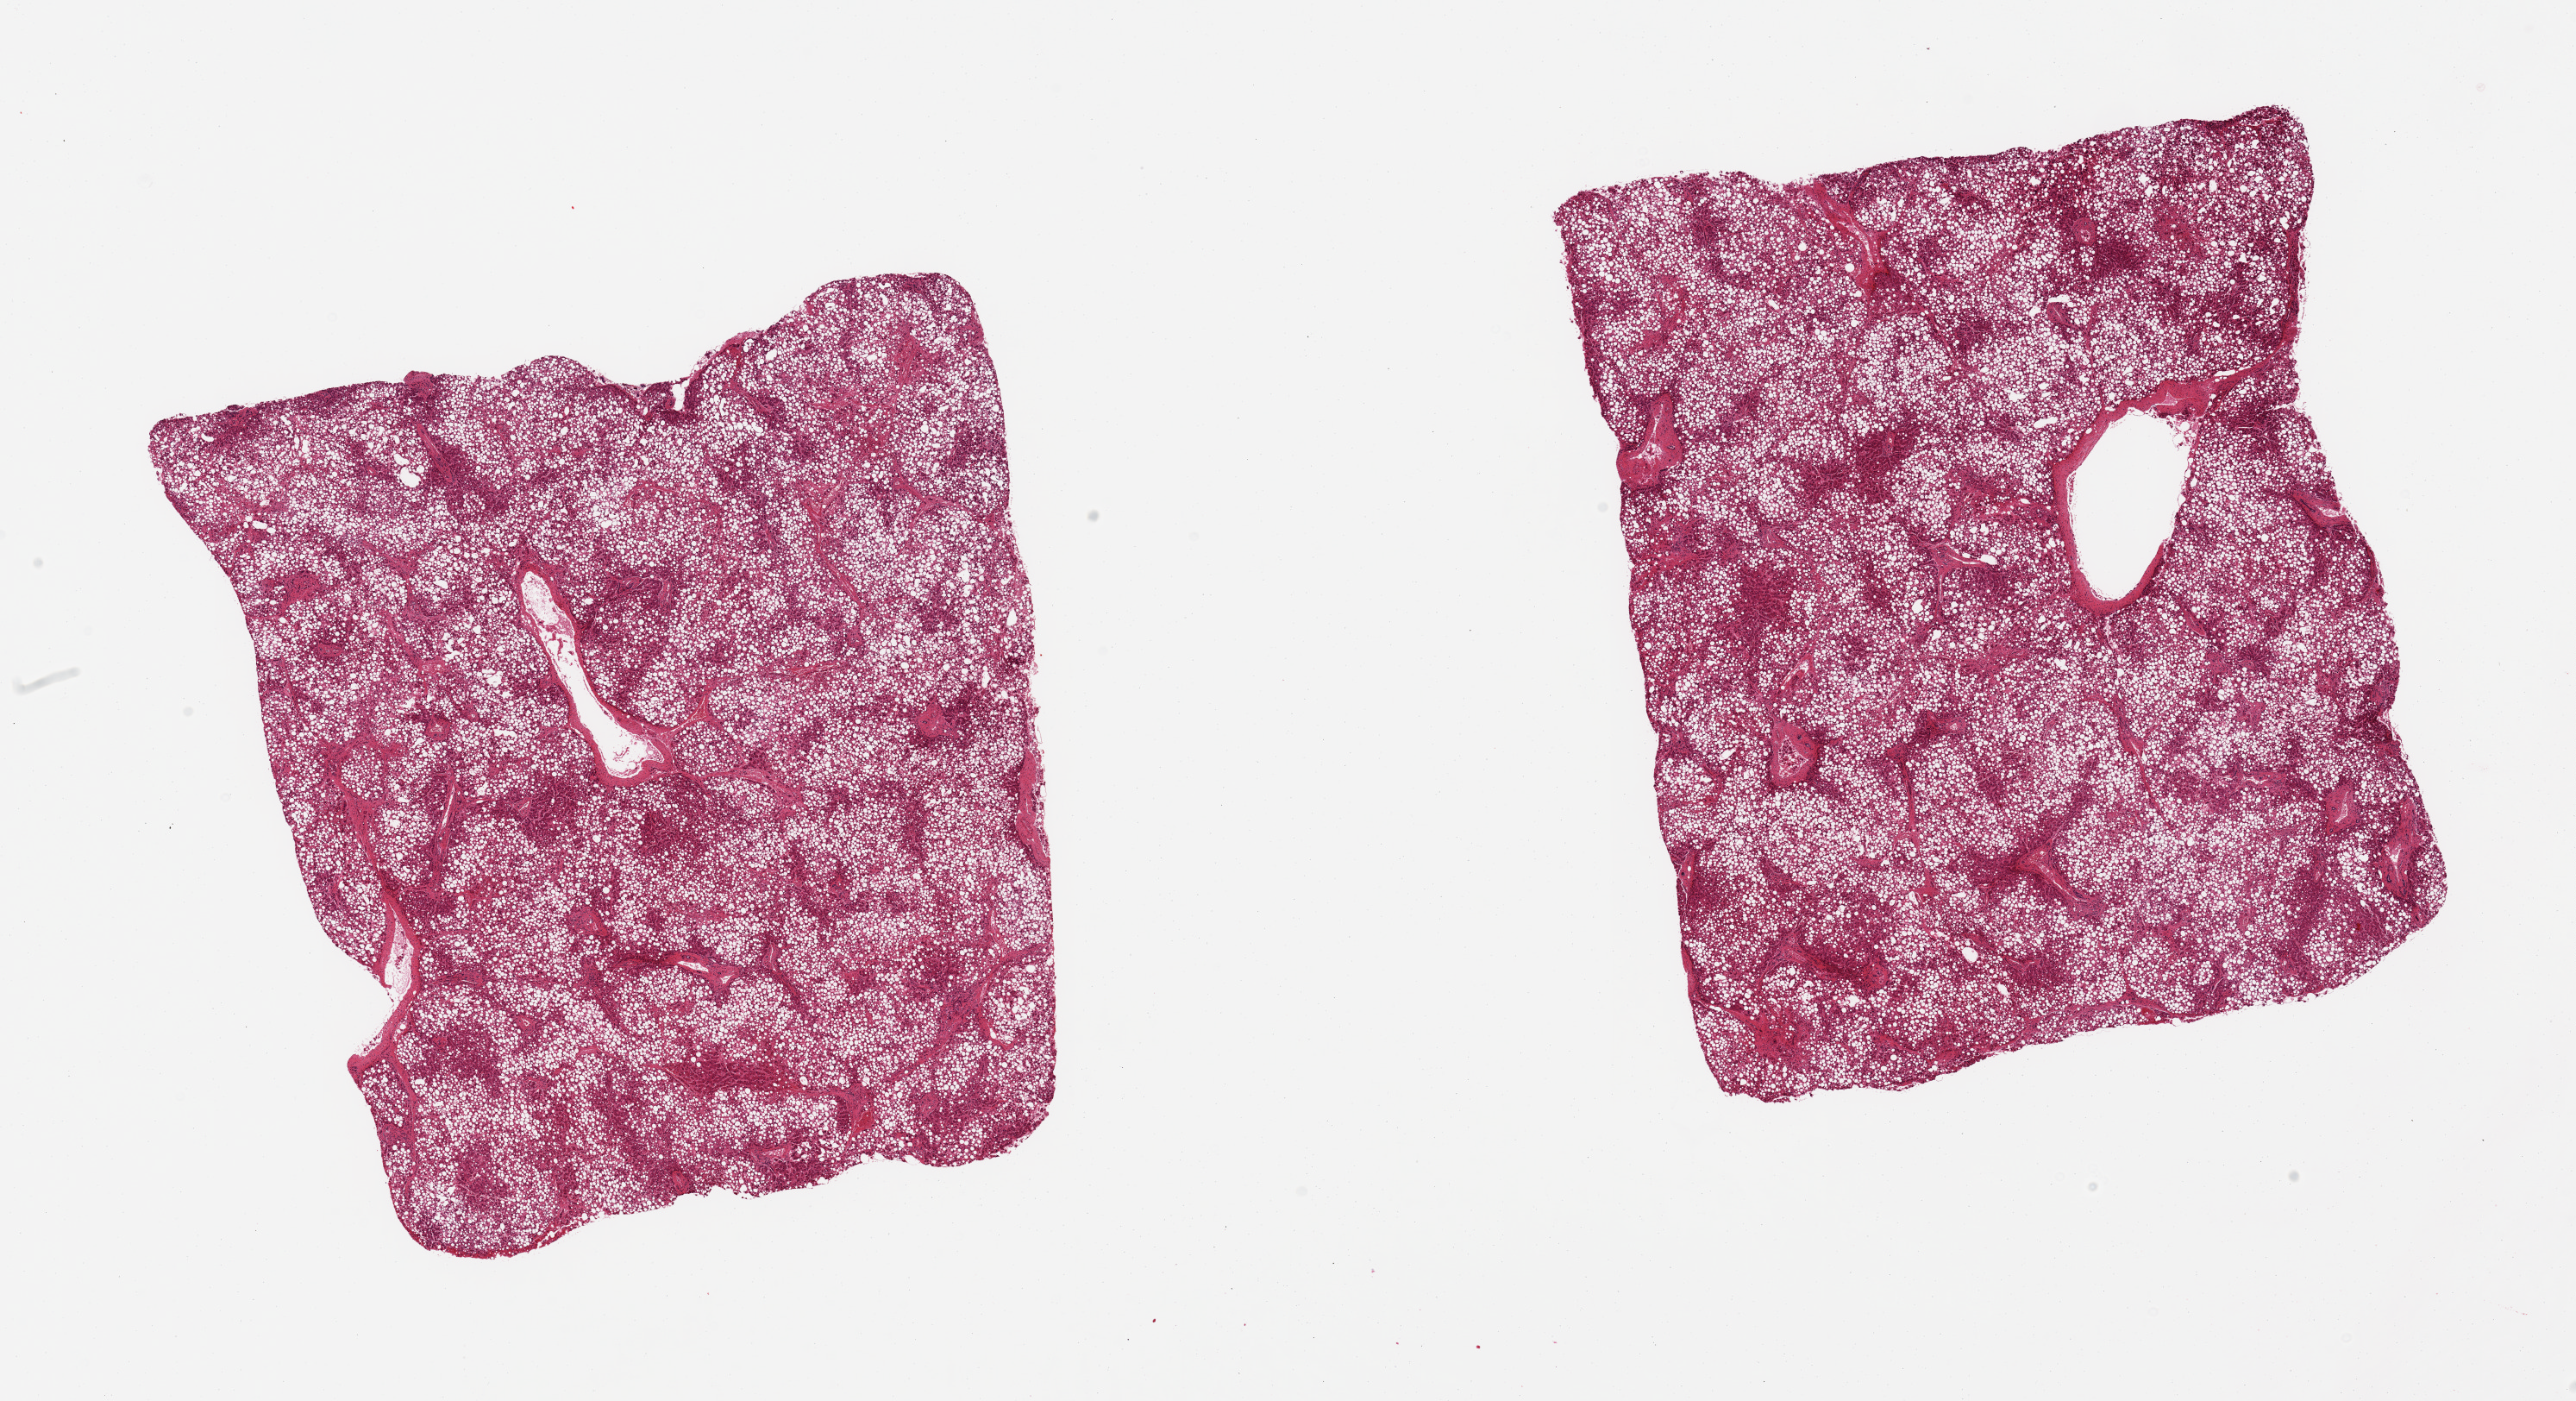
Haematoxylin and eosin whole-slide image — a low-resolution overview of the entire scanned area, about 23.6 x 12.8 mm (acquisition: 20x scan). PAXgene-fixed, paraffin-embedded tissue. Target tissue: liver. Donor tissue sample. Donor sex: male.
Review note (as recorded): 2 pieces, diffuse macrovesicular steatosis, ~90% parenchymal involvement.